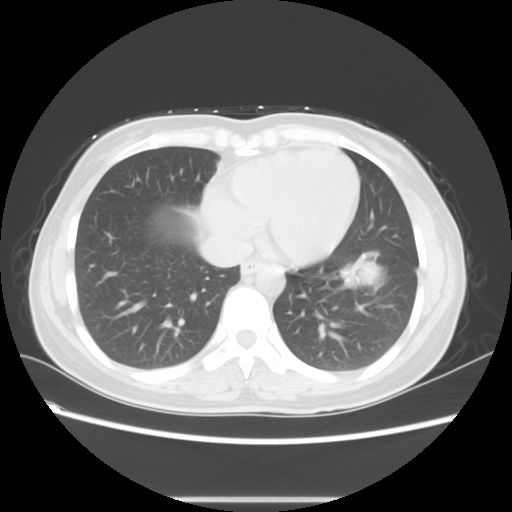
Chest CT, one axial slice; slice 21 of 56 in the series (ordered by position); reconstruction kernel STANDARD; 120 kVp; lung window (W 1500 / L -600 HU); 5 mm slice thickness; 512 × 512 image matrix, field of view 350 × 350 mm. Patient: female, 41 years. Case-level facts recorded for this patient, not image findings: clinical TNM (as recorded): T1c N3 M1b.
Annotated regions visible in this slice (rectangle marked by the reading radiologist):
- lung tumour (recorded histology: adenocarcinoma): box from (x=332, y=242) to (x=391, y=299) px